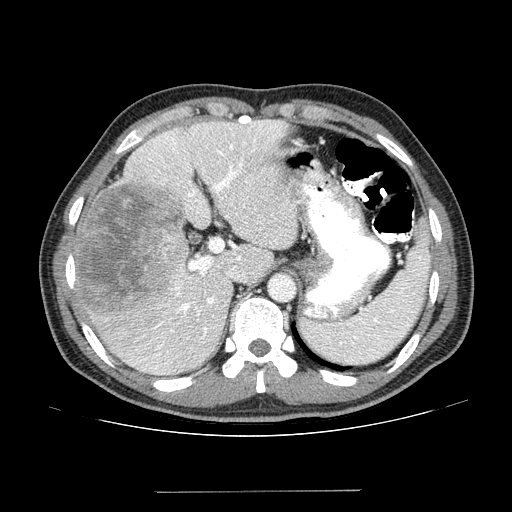
Contrast-enhanced abdominal CT (liver protocol), one axial slice; position 98 of 131 along the scan axis; one of 2 acquisitions stored at this slice position; soft-tissue window (W 400 / L 40 HU); 2.5 mm slice thickness; 512 × 512 image matrix, field of view 380 × 380 mm. Case-level facts recorded for this patient, not image findings: diagnosis: hepatocellular carcinoma (patient treated with transarterial chemoembolisation; whether this scan precedes or follows treatment is not stated here); TNM stage (as recorded): Stage-I; Child-Pugh class: A; tumour nodularity: uninodular; tumour size: 10.3 cm.
Structures marked on this image (semi-automatic segmentation, software-assisted and operator-edited):
- liver parenchyma outside the tumour (the mass and vessels are separate outlines, so this box may not span the whole liver): bounding box (x1, y1, x2, y2) in pixels: (72, 120, 296, 374)
- mass: (77, 182, 190, 318)
- liver vessels: (133, 122, 280, 370)